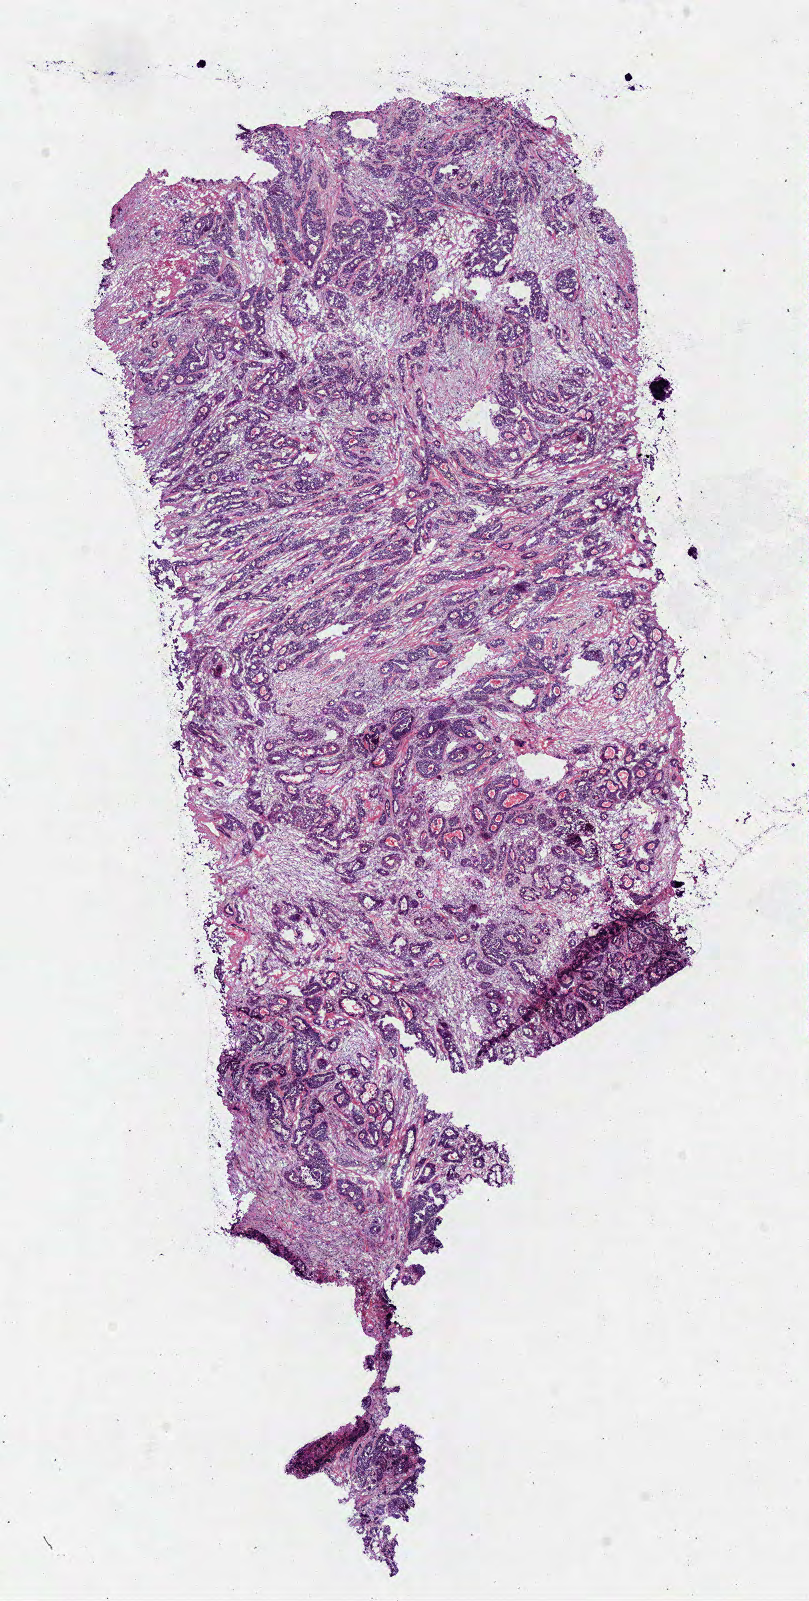
Whole-slide histology image, H&E, a low-resolution overview of the entire scanned area, about 6.4 x 12.6 mm. Frozen section from the bottom of the tissue portion. Rectum, primary tumour sample. Patient: male, age at initial diagnosis 53 years. Slide review estimates, as recorded: tumour cells 67%, tumour nuclei 80%.
Diagnosis: Adenocarcinoma in tubulovillous adenoma.